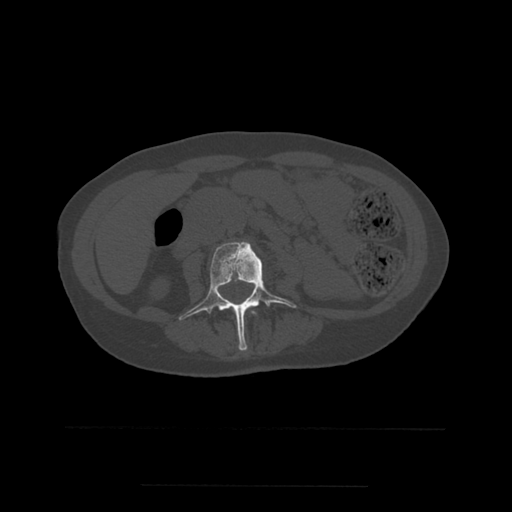
CT including the spine, one axial slice; slice 190 of 544 in the series (ordered by position); bone window (W 1800 / L 400 HU); 1.25 mm slice thickness; 512 × 512 image matrix, field of view 350 × 350 mm. Patient age 58 years. Case-level facts recorded for this patient, not image findings: primary cancer: lung.
Outlined on this slice (semi-automatic segmentation, software-assisted and operator-edited):
- L2 vertebra: bounding box (x1, y1, x2, y2) in pixels: (251, 311, 257, 315)
- L3 vertebra: (179, 242, 297, 351)